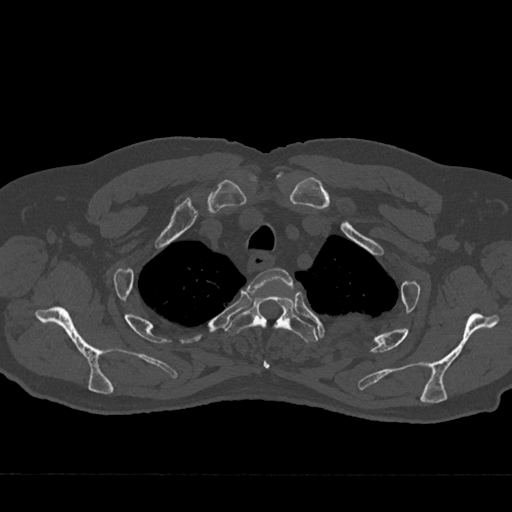
CT including the spine, one axial slice. Position 582 of 797 along the scan axis. Reconstruction kernel Br40s/3. 120 kVp. Bone window (W 1800 / L 400 HU). 0.5 mm slice thickness. 512 × 512 image matrix, field of view 377 × 377 mm. Patient: male, 75 years. From the clinical record (not read from this slice): primary cancer: renal; vertebrae with lytic lesions (as recorded): T4.
Outlined on this slice (semi-automatically segmented with operator editing):
- T2 vertebra: bounding box (x1, y1, x2, y2) in pixels: (249, 268, 294, 369)
- T3 vertebra: (227, 295, 318, 342)